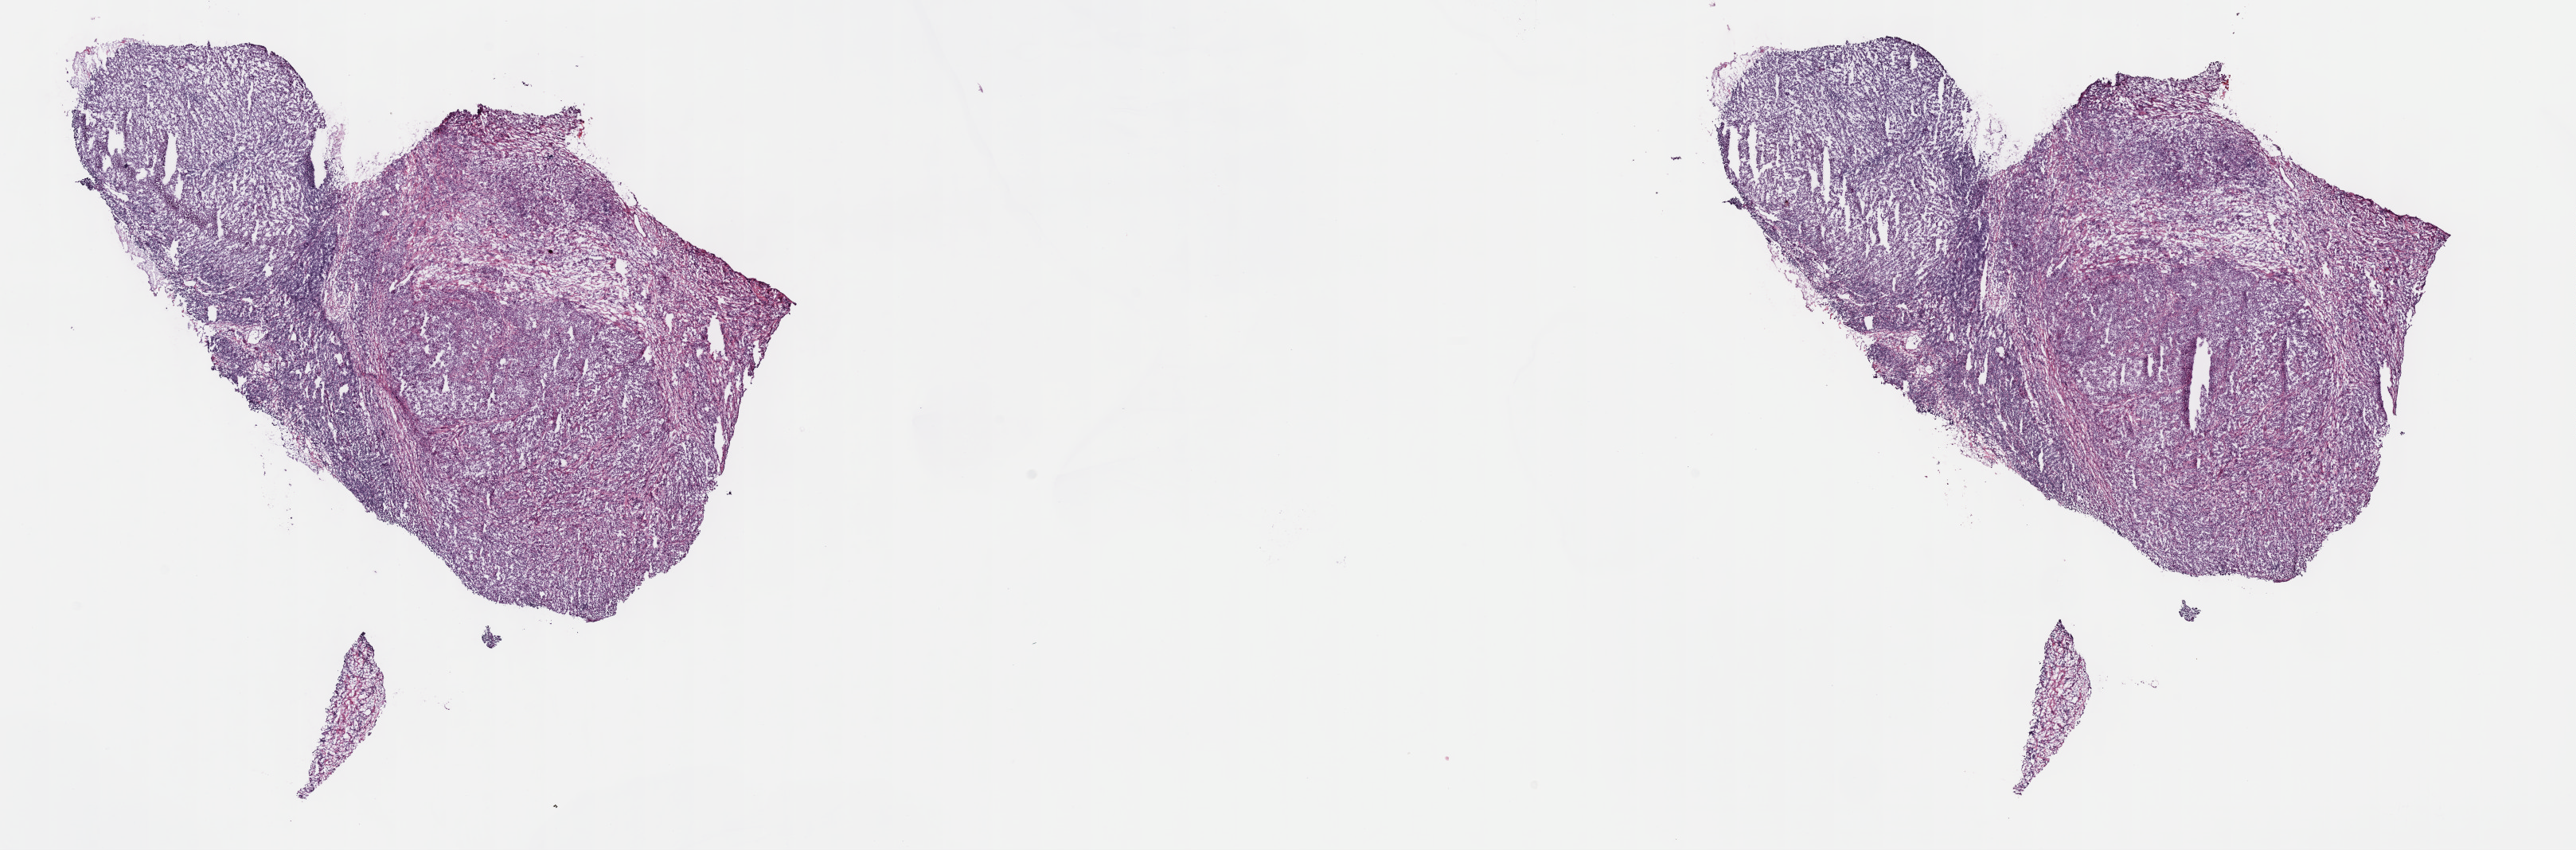
Digitized H&E-stained tissue section (whole slide), a low-resolution overview of the entire scanned area, about 26.2 x 8.6 mm (from a 40x scan), frozen section, metastatic tumour sample, sampled site: lymph nodes of axilla or arm. Female patient; age at initial diagnosis 40 years. Slide review estimates, as recorded: tumour cells 100%, tumour nuclei 75%, normal cells 0%, stromal cells 0%, necrosis 0%. Inflammatory infiltration, as recorded: lymphocyte infiltration 2%, monocyte infiltration 0%, neutrophil infiltration 0%.
* this section: metastatic tumour tissue
* patient diagnosis: Malignant melanoma, NOS